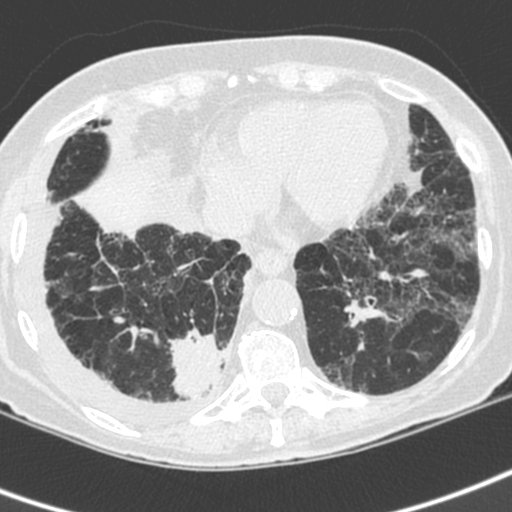
Chest CT (low-dose screening protocol), one axial image, baseline annual screen, lung window (W 1500 / L -600 HU), slice 139 of 192 in the series. Female, age 73 years at enrolment. Current smoker at enrolment.
• Expert reader's lesion annotation, box from (x=156, y=318) to (x=235, y=406) px.
• The exam's reader record, not a measurement of the box and not confirmed to be the same lesion: non-calcified nodule or mass ≥4 mm, right lower lobe, 35 × 30 mm, spiculated (stellate) margins, soft tissue attenuation.